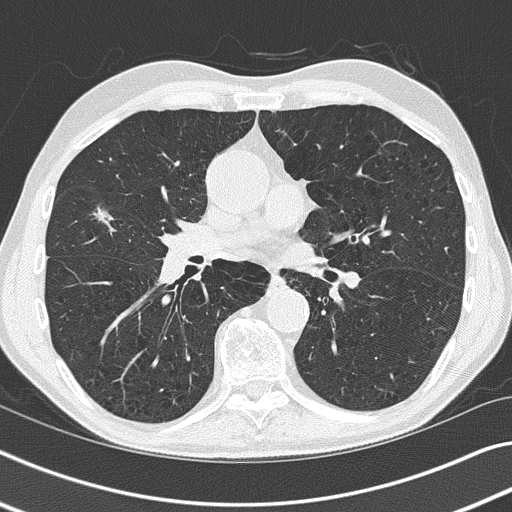
Low-dose screening chest CT, axial slice; baseline screening round; lung window (W 1500 / L -600 HU); 2 mm slice thickness; lung (sharp) reconstruction kernel (B50f). Male participant, aged 73 years at enrolment.
• Lesion marked by an expert reader, box from (x=76, y=192) to (x=129, y=241) px.
• The screening reader recorded 3 non-calcified nodules or masses ≥4 mm on this exam (right upper lobe, right middle lobe, right upper lobe); which of them this box marks is not recorded.
• Official screen result: positive, change unspecified: nodule(s) >= 4 mm or enlarging nodule(s), mass(es), or other non-specific abnormalities suspicious for lung cancer.
• Later outcome: lung cancer diagnosed 45 days after this screen — bronchiolo-alveolar adenocarcinoma, NOS, right middle lobe, well differentiated (G1), stage IA (AJCC 6th edition), 11 mm at pathology.